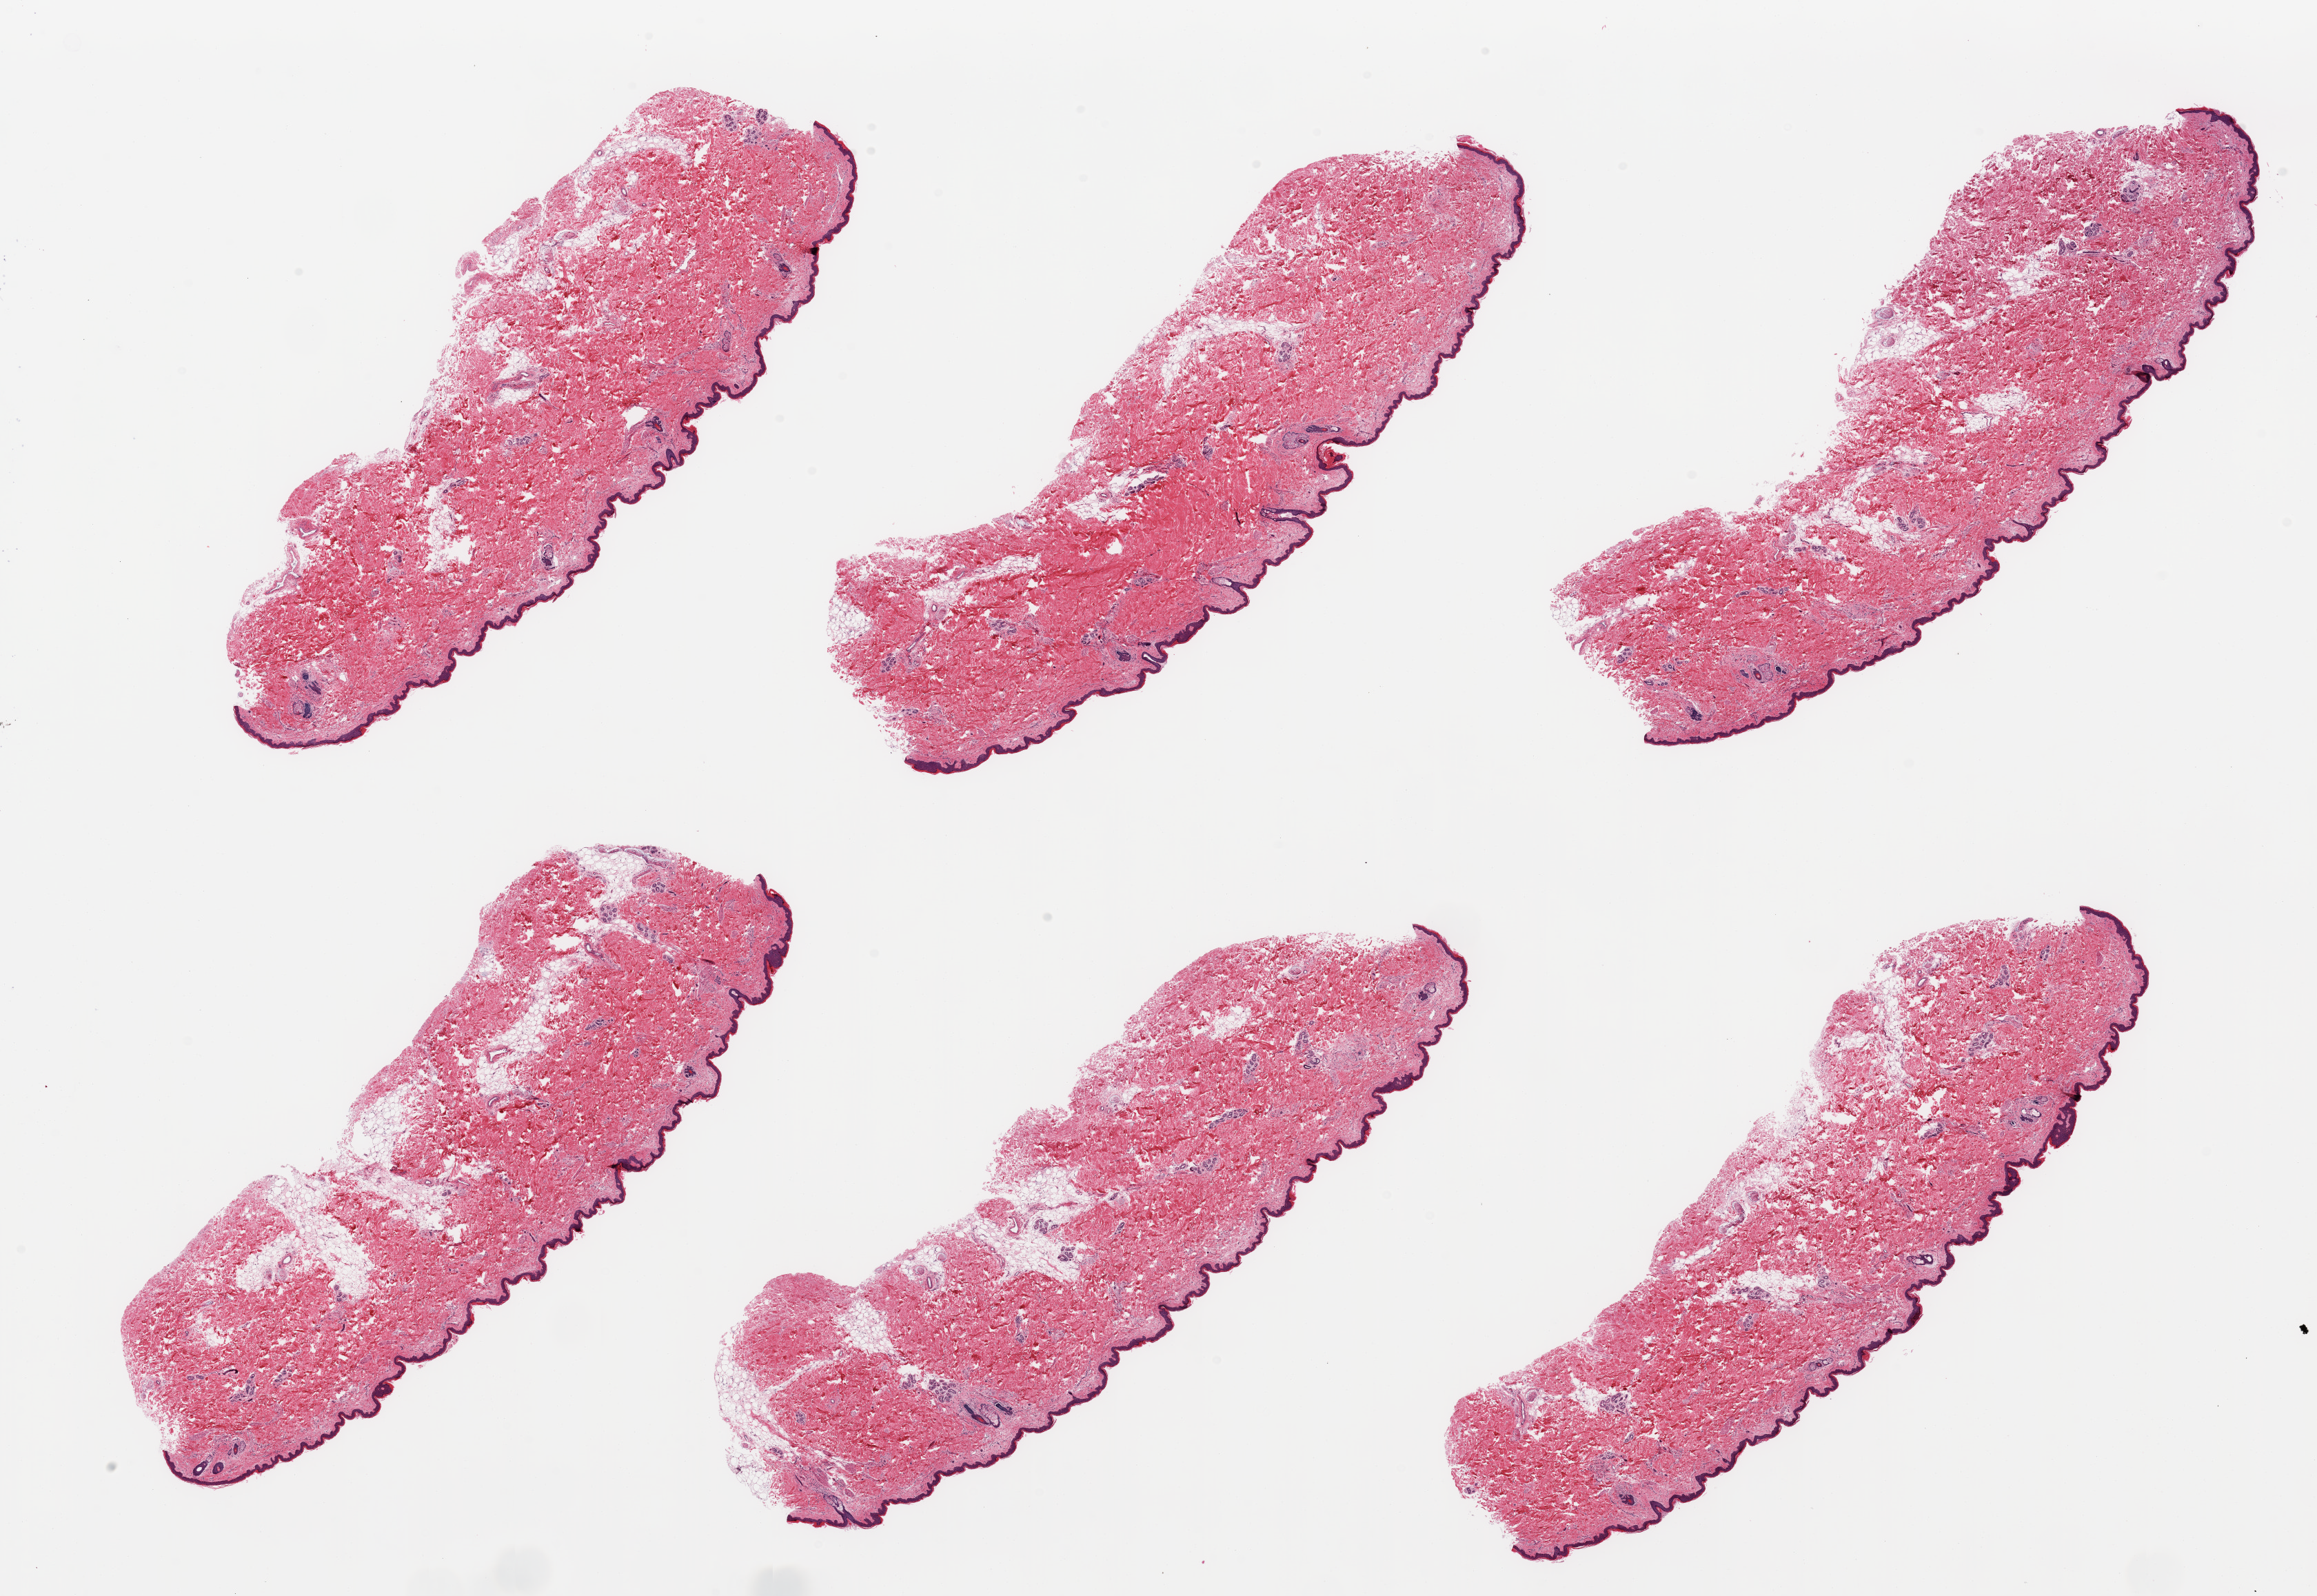
Haematoxylin and eosin whole-slide image — shown as a low-resolution overview of the whole scanned area (about 26.6 x 18.3 mm, acquisition: 20x scan). PAXgene-fixed paraffin-embedded (PFPE) section. Section of skin of lower leg (target tissue). Donor tissue sample. Female donor.
Review note (as recorded): 6 pieces; includes up to ~10% mostly internal fat, epidermis measures 36 microns.